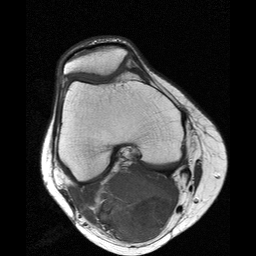
MRI of an extremity soft-tissue mass, one axial slice. Slice 10 of 25 in the series (ordered by position). 256 × 256 image matrix. Female patient. From the clinical record (not read from this slice): histological type: liposarcoma; site of the primary tumour: right thigh.
Structures marked on this image (expert manual segmentation):
- gross tumour volume (mass): bounding box [x1, y1, x2, y2] px = [91, 172, 172, 242]